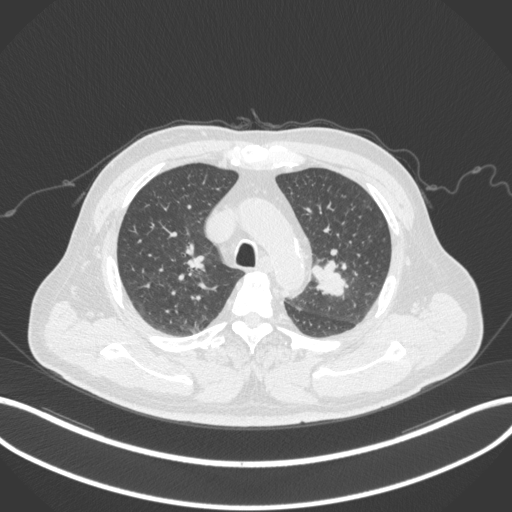
Chest CT, one axial slice; position 223 of 286 along the scan axis; reconstruction kernel B31f; 120 kVp; lung window (W 1500 / L -600 HU); 1 mm slice thickness; 512 × 512 image matrix. Male patient, age 67 years. Case-level facts recorded for this patient, not image findings: clinical TNM (as recorded): T2a N1 M0; histopathological grade: G3.
Structures marked on this image (rectangle marked by the reading radiologist):
- lung tumour (recorded histology: adenocarcinoma): bounding box (x1, y1, x2, y2) in pixels: (309, 257, 350, 298)